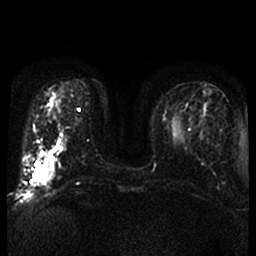
Breast MRI, one axial slice; position 15 of 52 along the scan axis; diffusion-weighted series; image 2 of 4 stored at this slice position (different b-values; order by instance number); 1.5 T; 4 mm slice thickness; 256 × 256 image matrix, field of view 320 × 320 mm. Female patient.
Outlined on this slice (manually delineated by an expert):
- tumour on diffusion-weighted imaging: bounding box <33,163,53,182> (left, top, right, bottom; pixels)